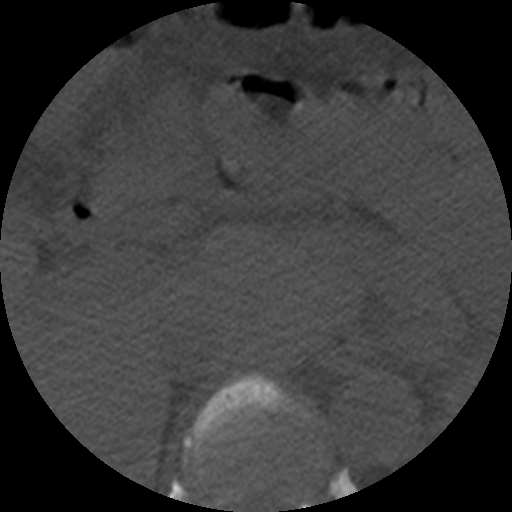
CT including the spine, one axial slice; slice 253 of 508 in the series (ordered by position); 120 kVp; bone window (W 1800 / L 400 HU); 512 × 512 image matrix, field of view 160 × 160 mm. Patient age 57 years. From the clinical record (not read from this slice): primary cancer: prostate.
Structures marked on this image (semi-automatically segmented with operator editing):
- T11 vertebra: bounding box <184,372,312,512> (left, top, right, bottom; pixels)